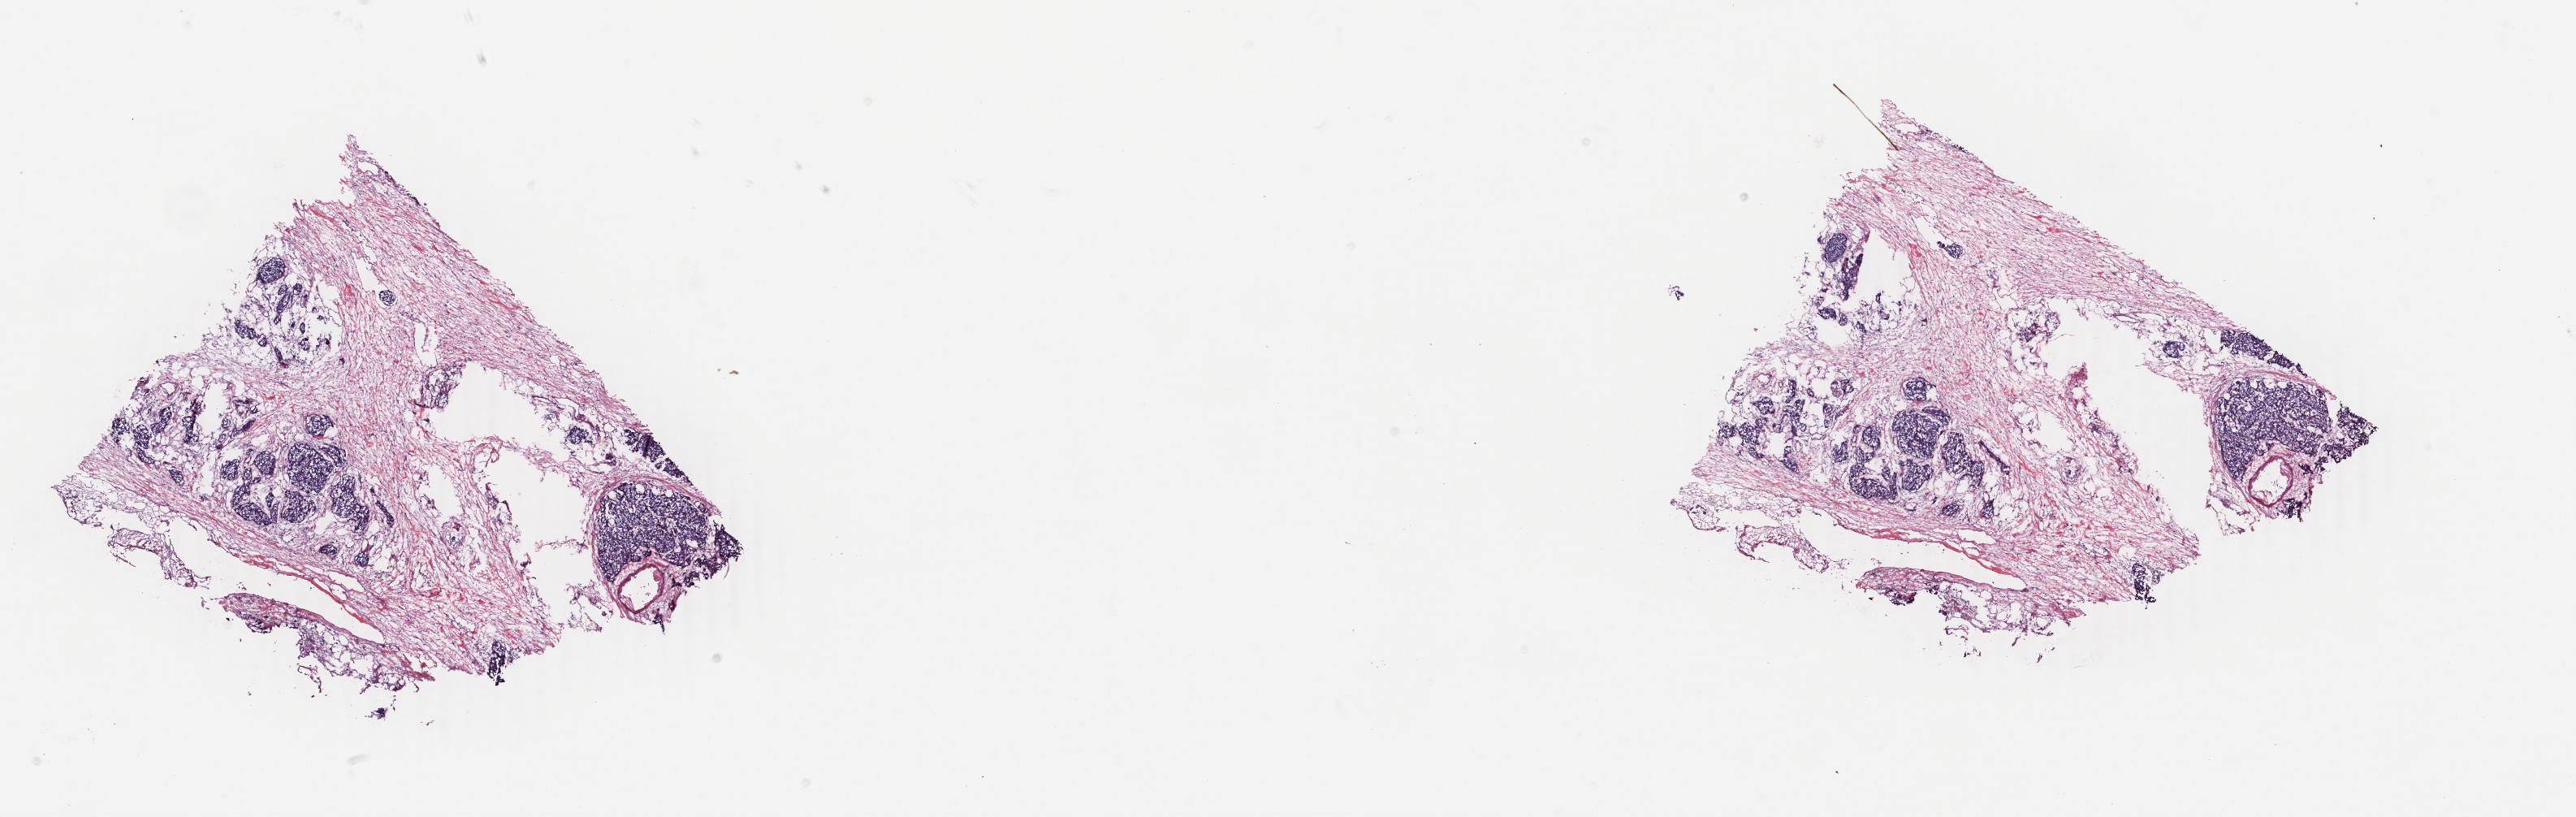
Digitized H&E-stained tissue section (whole slide) — shown as a low-resolution overview of the whole scanned area (about 25.2 x 8.0 mm, slide scanned at 40x), frozen section from the top of the tissue portion, bladder, primary tumour sample. Male, age 75 years at initial diagnosis. Slide review estimates, as recorded: tumour cells 70%, tumour nuclei 70%.
Histologic diagnosis: Transitional cell carcinoma.